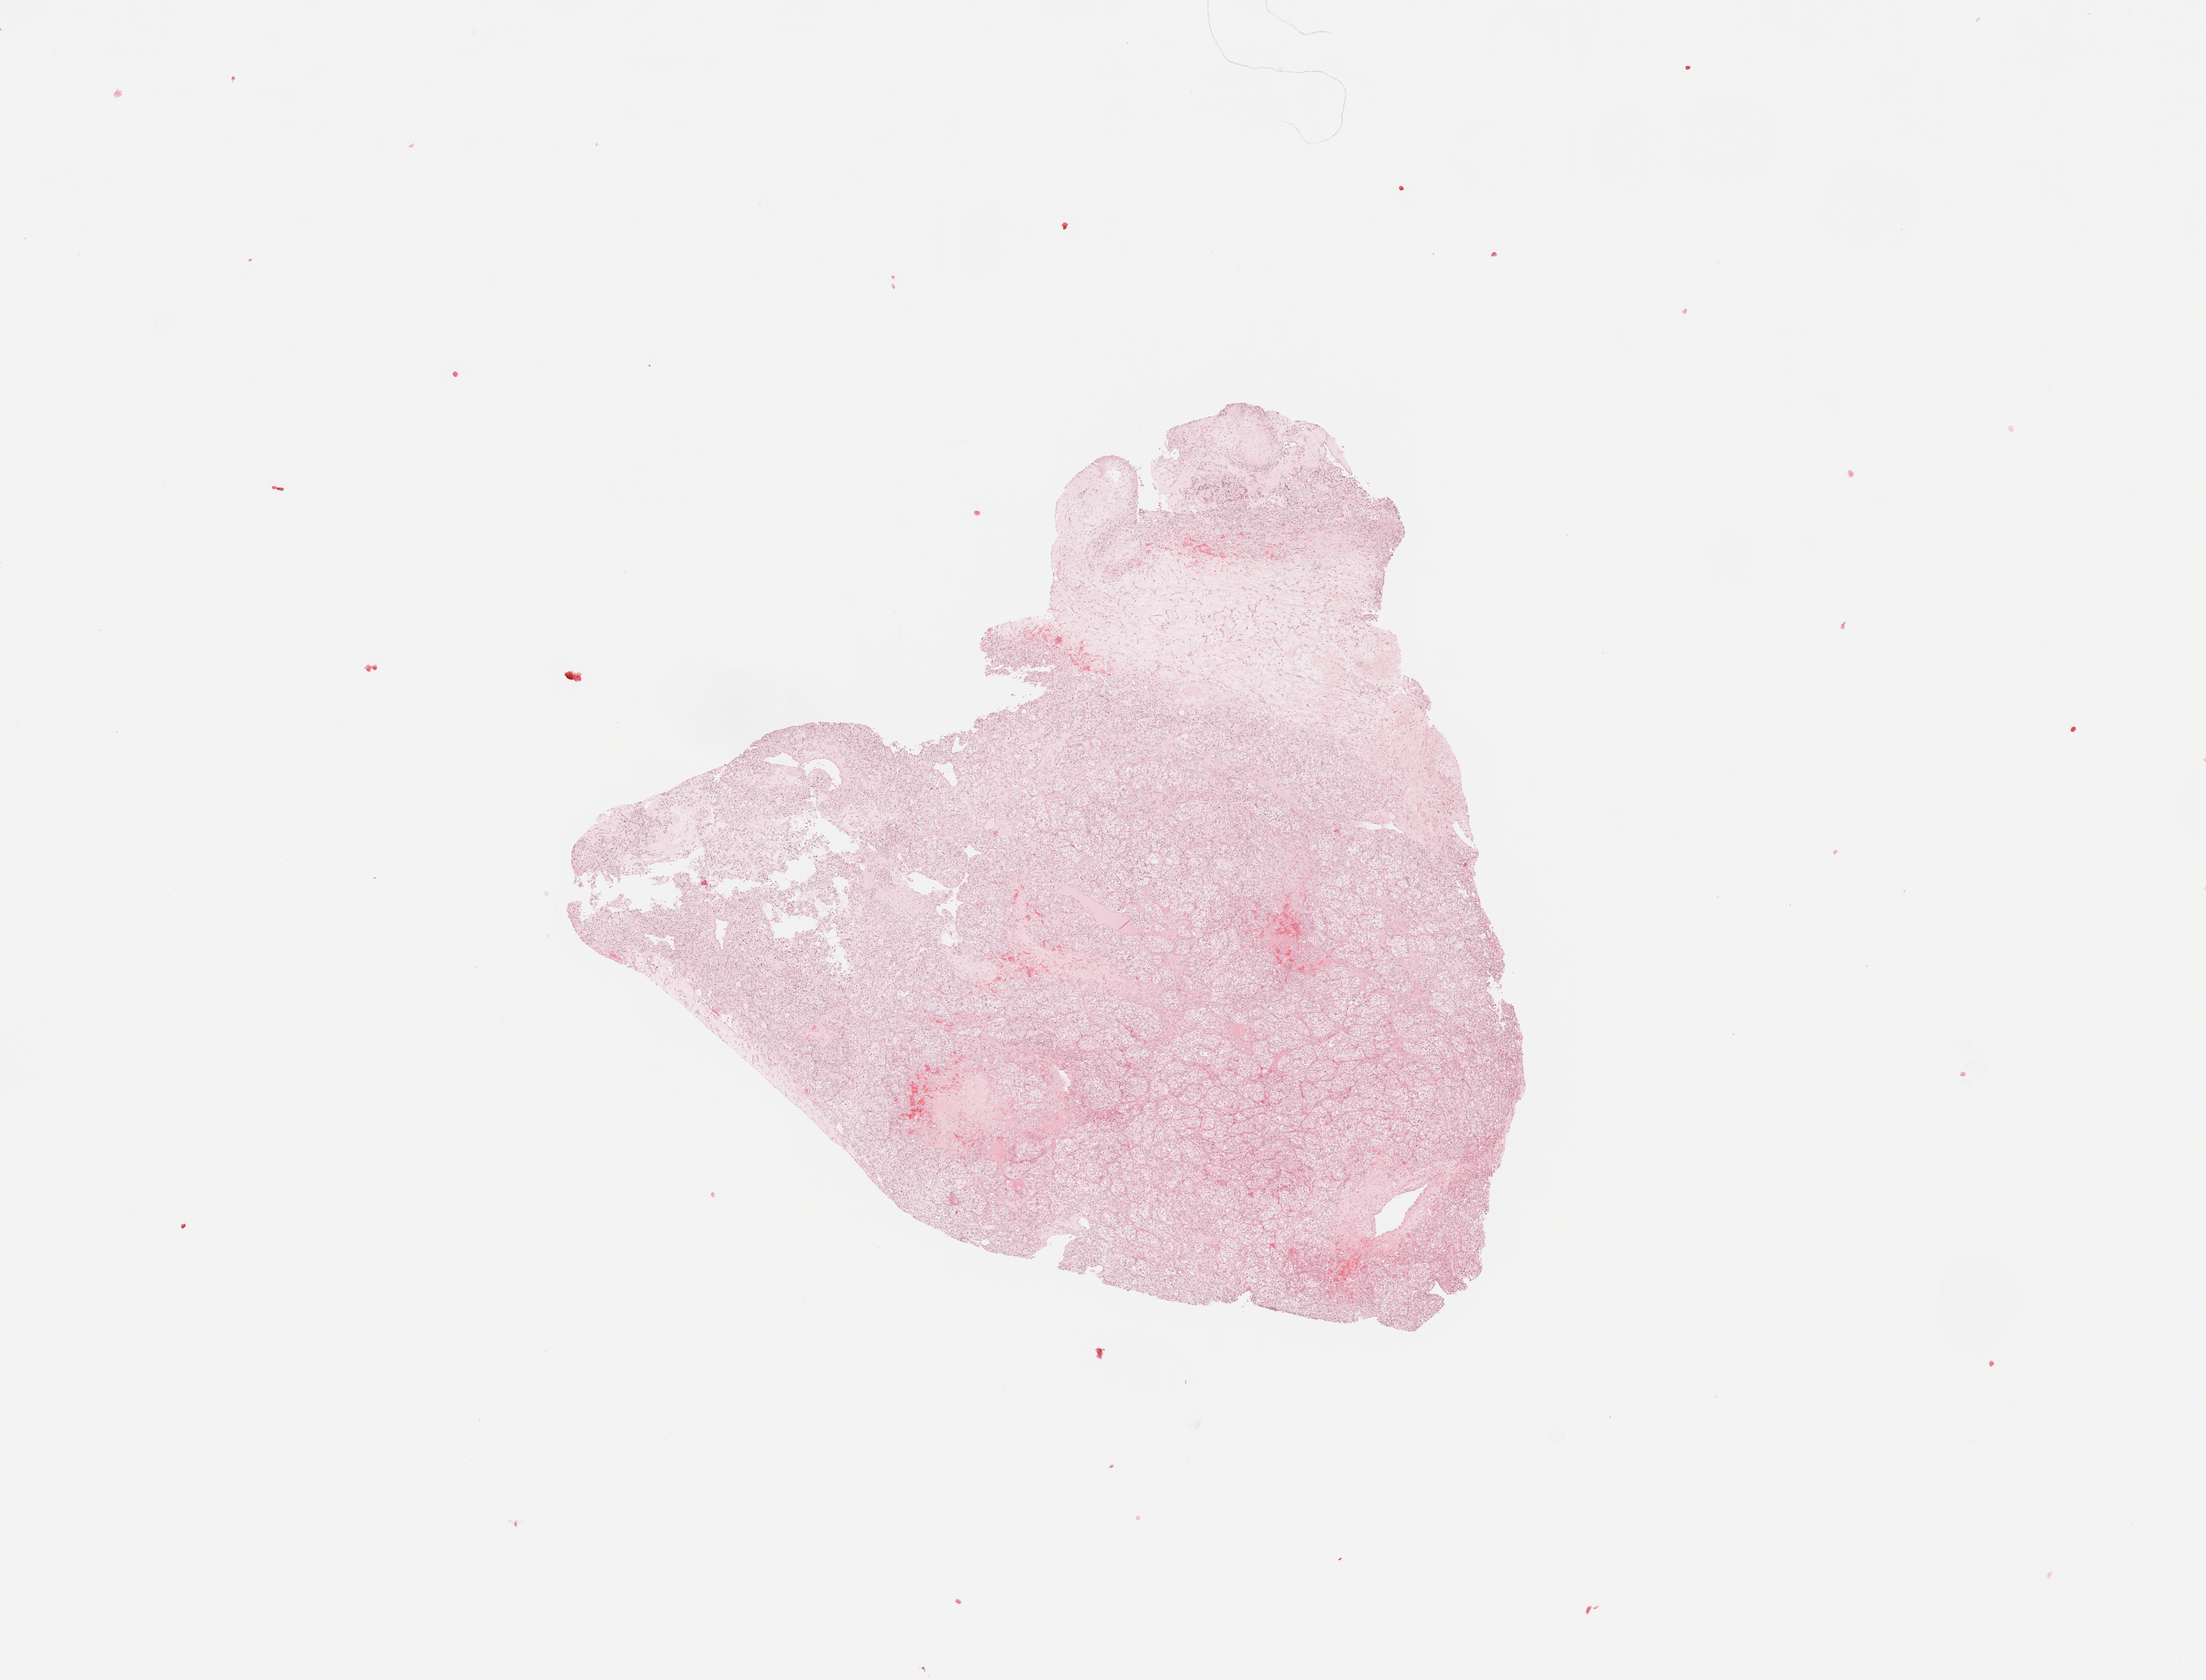
Digitized Hematoxylin and eosin (H&E) stained tissue section (whole slide), low-resolution overview of the scanned area, about 13.8 x 10.5 mm (slide scanned at 20x), tumour tissue sample, sampled site: kidney. Male, 51 y/o. Histologic grade: G3 (poorly differentiated). Slide review estimates, as recorded: tumour nuclei 85%, necrosis 2%.
AJCC pathologic stage: III. Histologic diagnosis: Renal cell carcinoma, NOS.